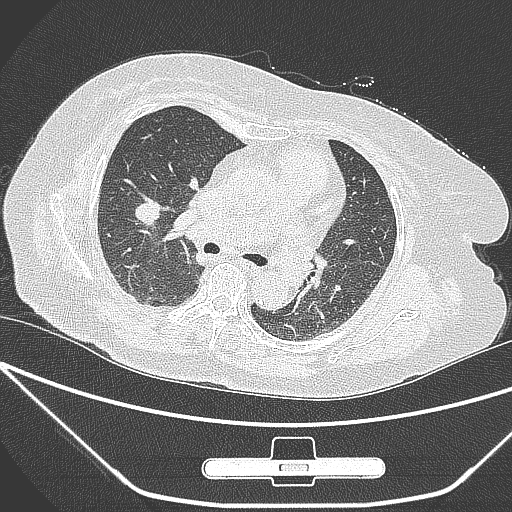
Chest CT, one axial slice. Slice 159 of 245 in the series (ordered by position). 120 kVp. Lung window (W 1500 / L -600 HU). 1 mm slice thickness. 512 × 512 image matrix, field of view 365 × 365 mm. Patient: female, 65 years. Case-level facts recorded for this patient, not image findings: clinical TNM (as recorded): T1c N0 M0.
Outlined on this slice (bounding box drawn by a radiologist):
- lung tumour (recorded histology: adenocarcinoma): box from (x=129, y=198) to (x=171, y=242) px